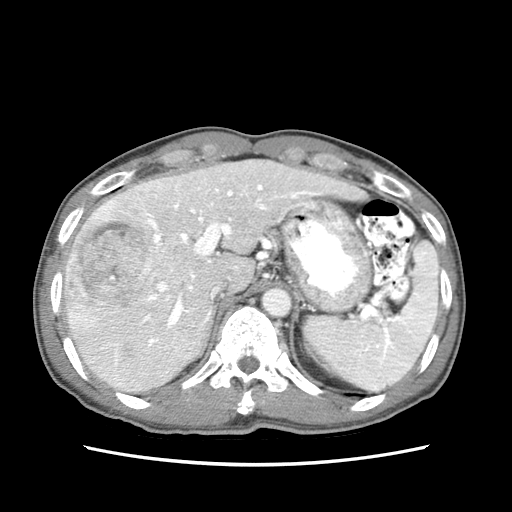
Contrast-enhanced abdominal CT (liver protocol), one axial slice. Slice 50 of 79 in the series (ordered by position). Reconstruction kernel STANDARD. 120 kVp. Soft-tissue window (W 400 / L 40 HU). 2.5 mm slice thickness. 512 × 512 image matrix. Case-level facts recorded for this patient, not image findings: diagnosis: hepatocellular carcinoma (patient treated with transarterial chemoembolisation; whether this scan precedes or follows treatment is not stated here); TNM stage (as recorded): Stage-IIIB.
Annotated regions visible in this slice (semi-automatically segmented with operator editing):
- liver parenchyma outside the tumour (the mass and vessels are separate outlines, so this box may not span the whole liver): box from (x=62, y=158) to (x=366, y=392) px
- mass: (x=65, y=205)–(x=161, y=328)
- liver vessels: (x=104, y=169)–(x=302, y=347)